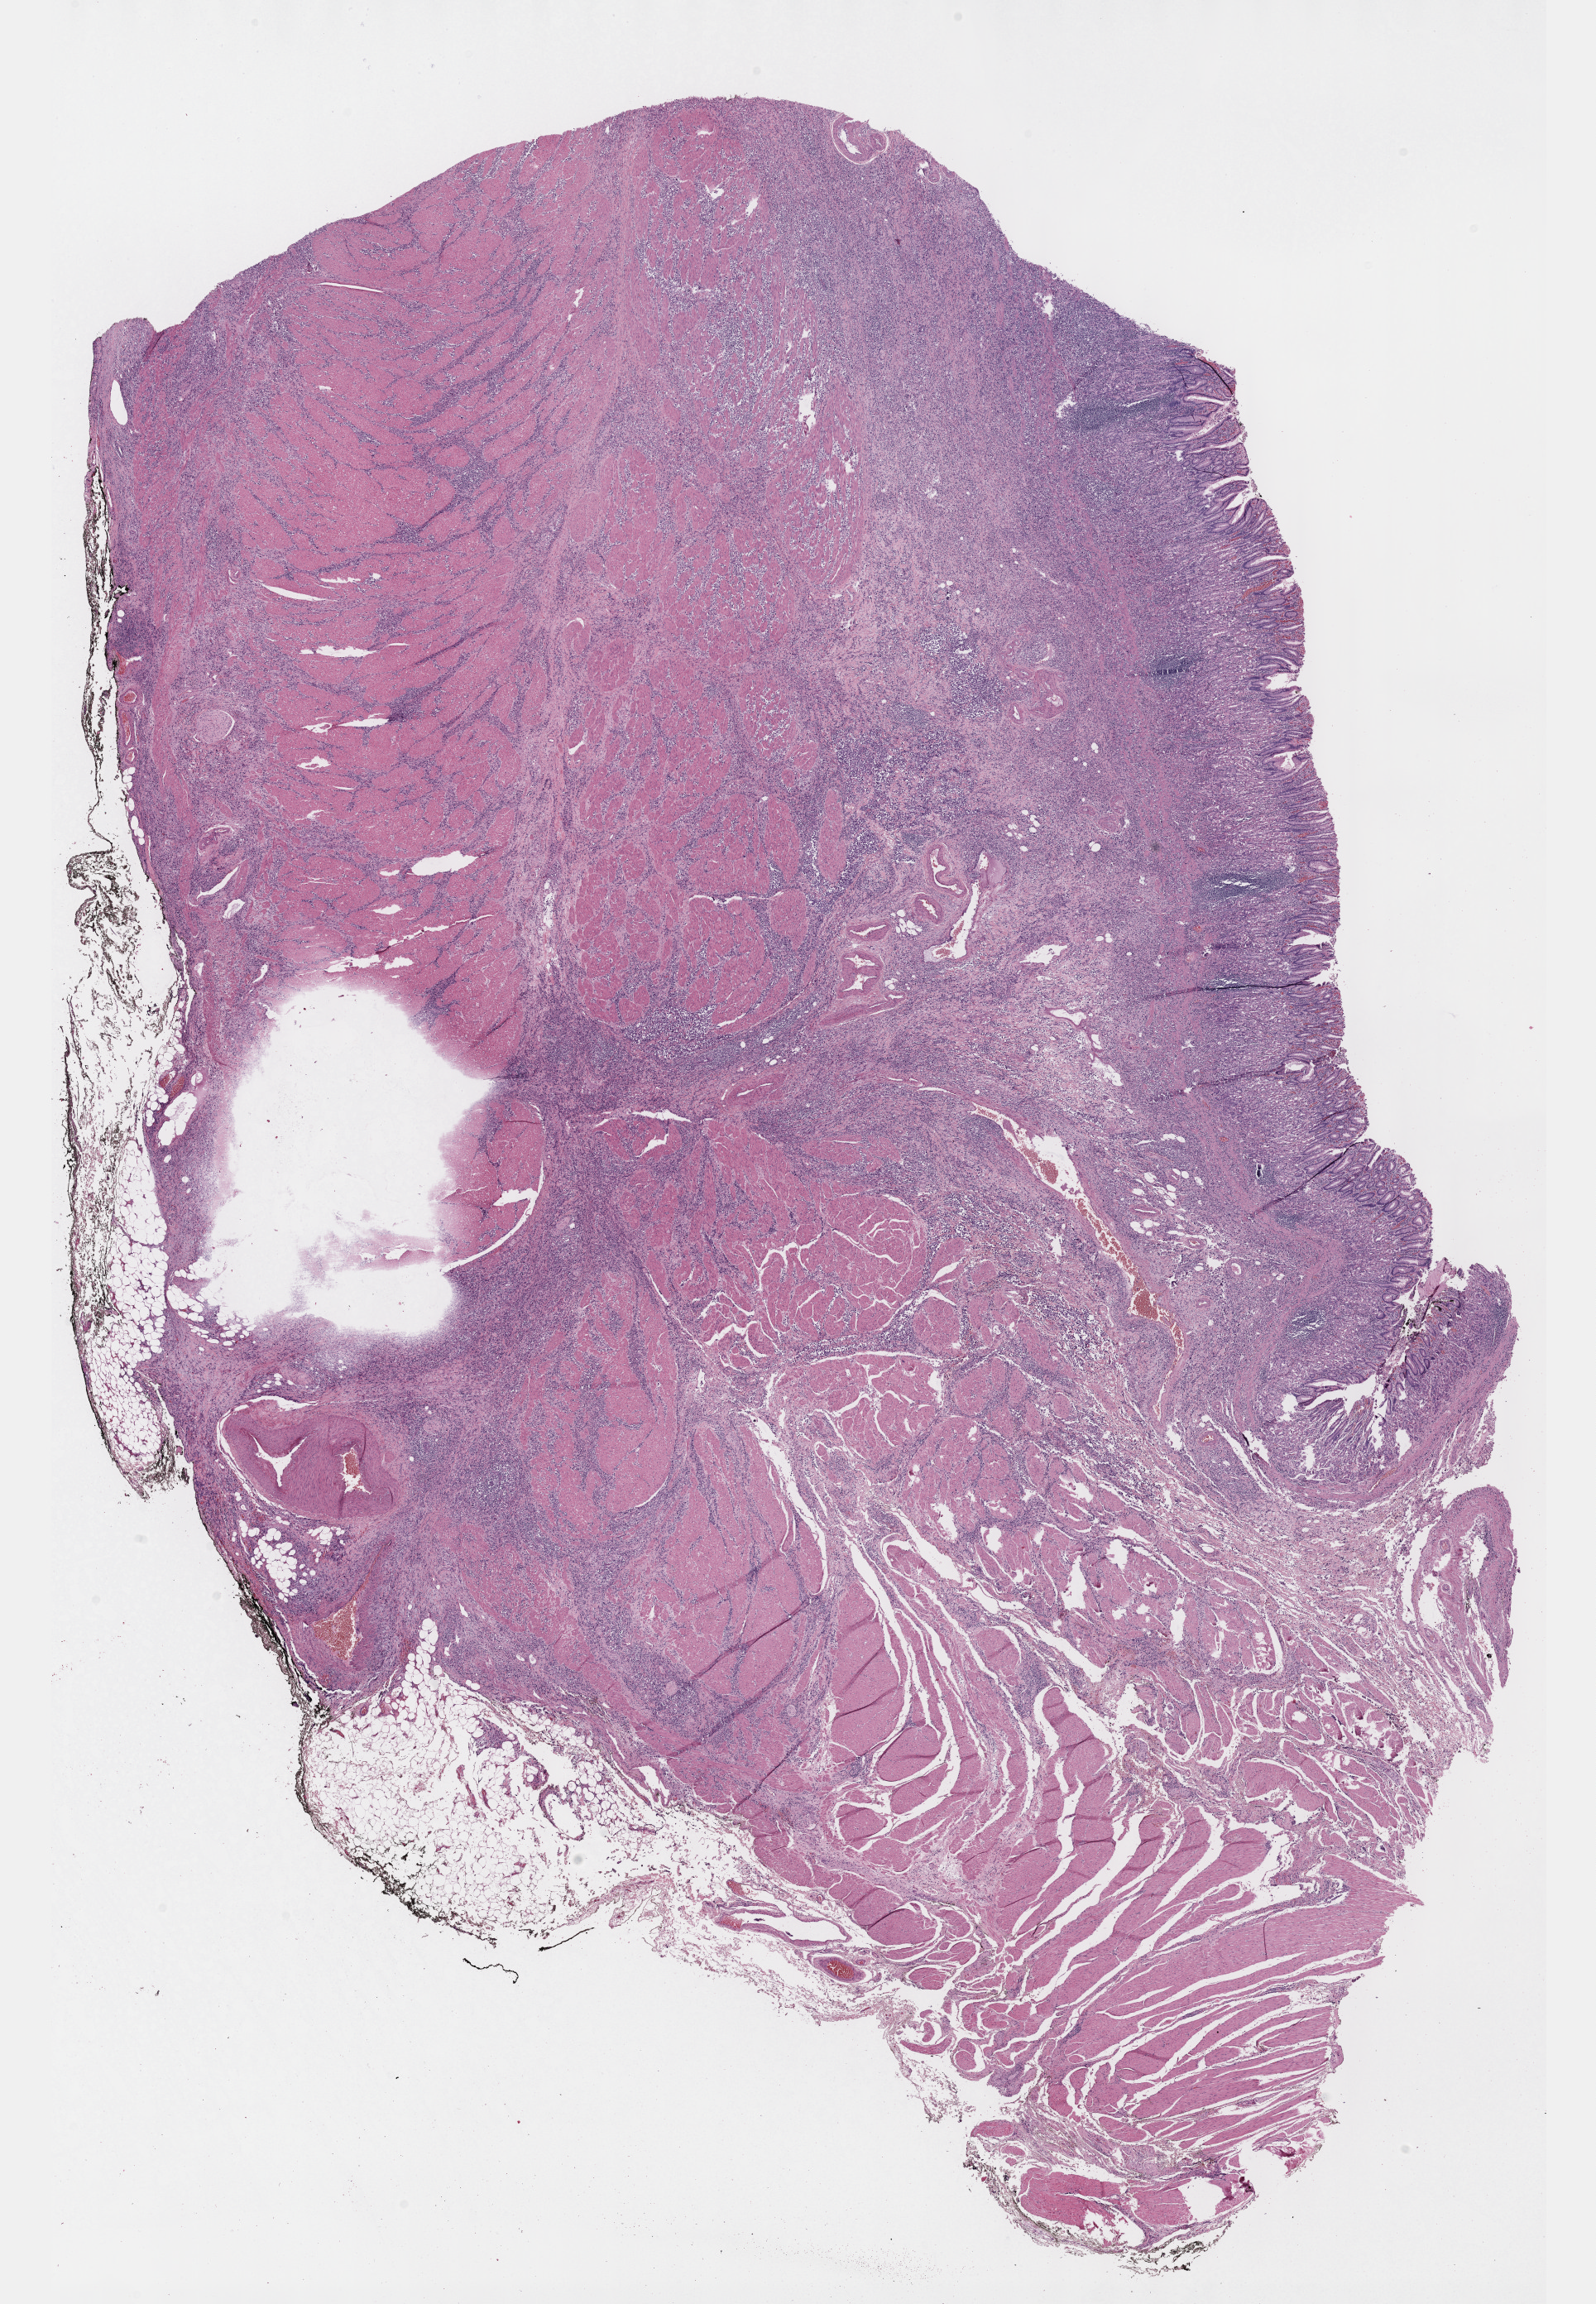
Hematoxylin and eosin (H&E) stained whole-slide image — whole scanned area (about 15.6 x 22.5 mm, slide scanned at 40x) shown as a low-resolution overview; formalin-fixed paraffin-embedded (FFPE) diagnostic section; sample: primary tumour, stomach. Patient: male, age at initial diagnosis 70 years.
Histologic diagnosis: Signet ring cell carcinoma (gastric antrum).